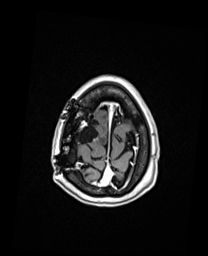
Brain MRI from a brain-tumour surgery series, one axial slice. Slice 30 of 192 in the series (ordered by position). T1-weighted post-contrast. 208 × 256 image matrix, field of view 208 × 256 mm. From the clinical record (not read from this slice): histopathology: Oligodendroglioma; WHO grade: 3; IDH mutation: yes; tumour location: Right Frontal.
Outlined on this slice (manually delineated by an expert):
- previous resection cavity: bounding box <73,116,95,142> (left, top, right, bottom; pixels)